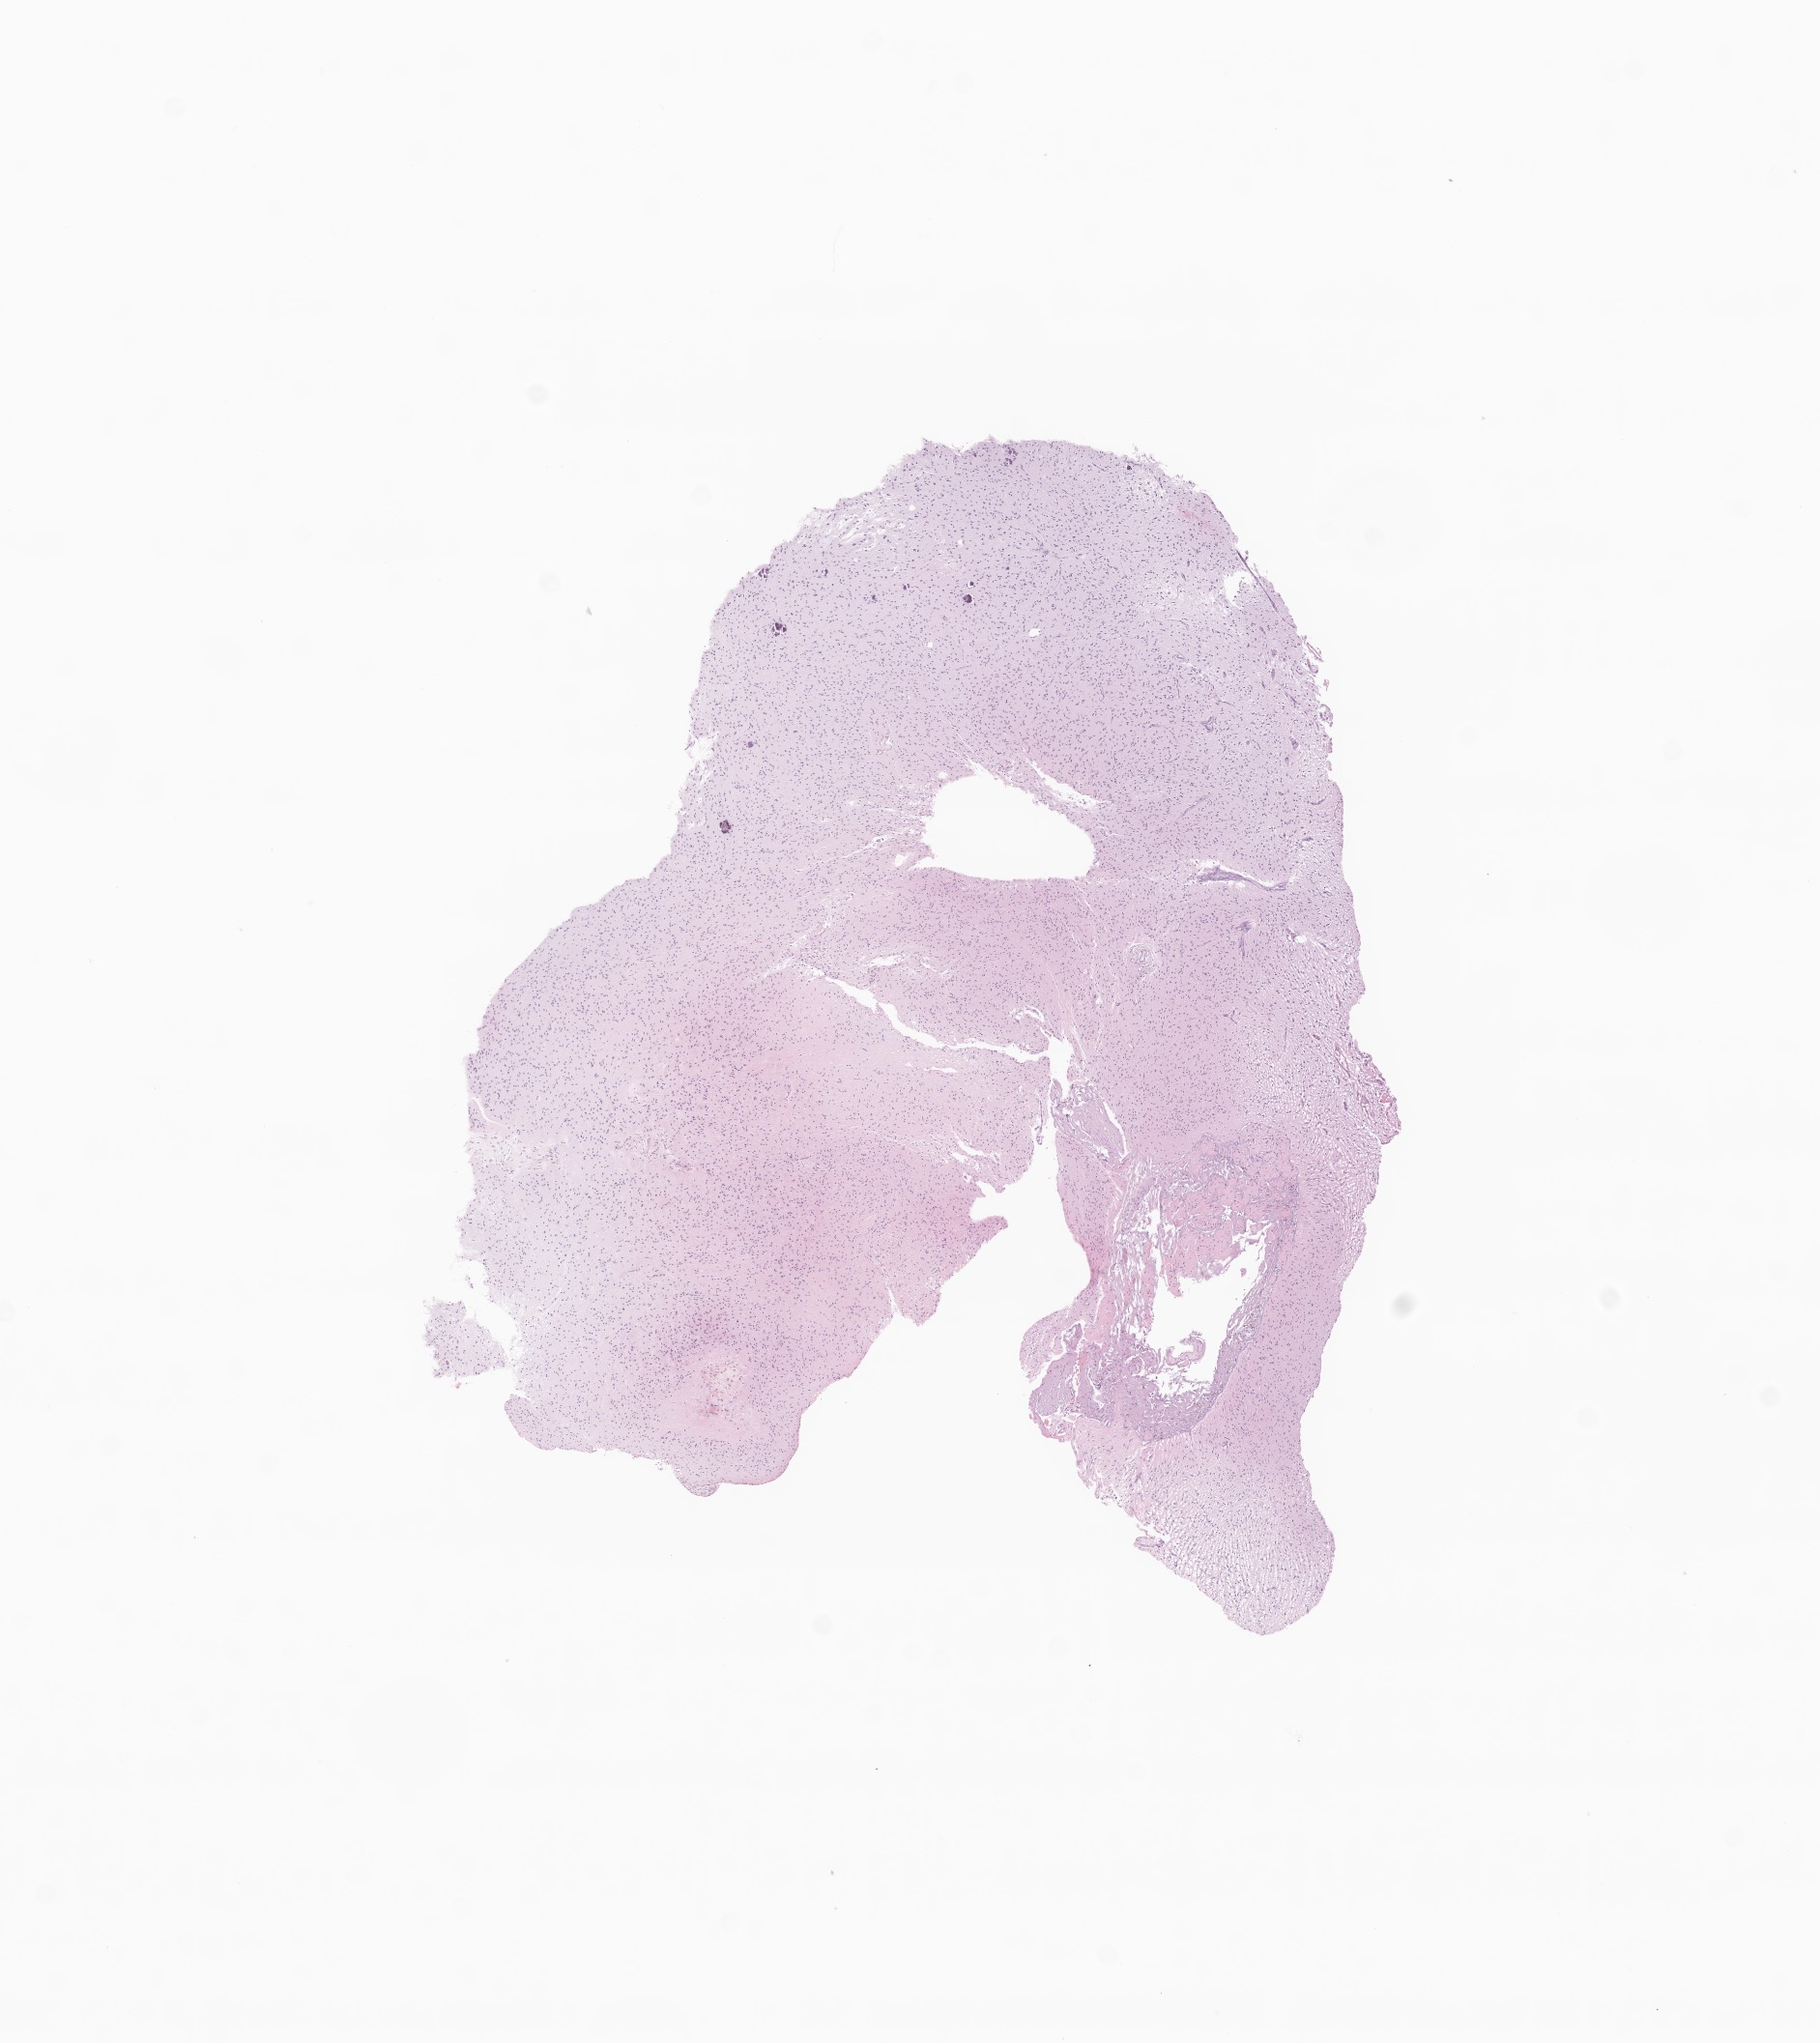
H&E whole-slide image of tumor tissue from the brain, whole scanned area (about 7.9 x 8.9 mm) shown as a low-resolution overview. Formalin-fixed paraffin-embedded section. Patient male; age 260 months (21 years 8 months).
Recorded diagnosis: Glioma, malignant.